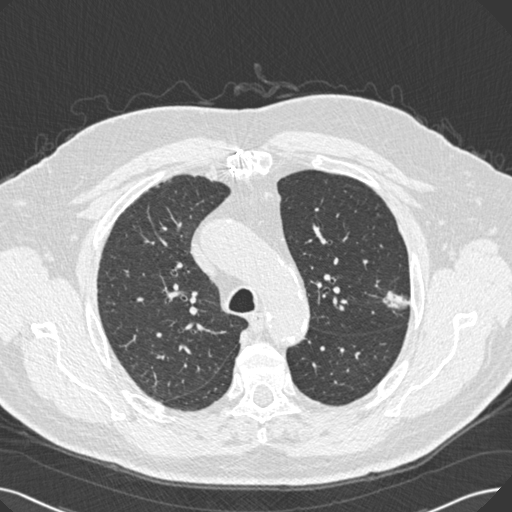
Low-dose screening chest CT, one axial slice; reconstruction kernel B30f; 120 kVp; lung window (W 1500 / L -600 HU); 1 mm slice thickness; 512 × 512 image matrix, field of view 370 × 370 mm.
Annotated regions visible in this slice (manually delineated by an expert):
- lesion 1 (tumor, upper lobe of left lung): bounding box <383,291,410,313> (left, top, right, bottom; pixels)